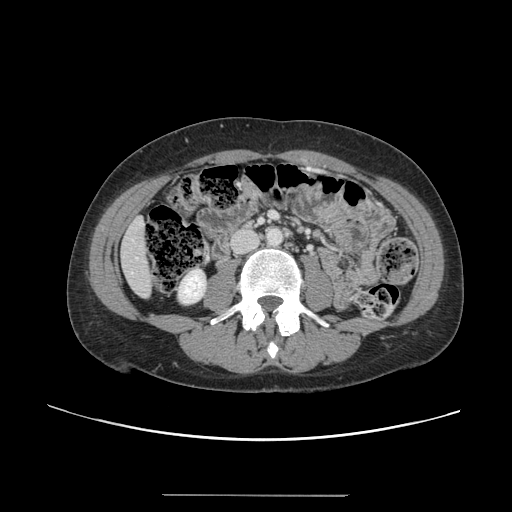
Contrast-enhanced abdominal CT, one axial slice; position 24 of 144 along the scan axis; intravenous contrast given; soft-tissue window (W 400 / L 40 HU); 2.5 mm slice thickness; 512 × 512 image matrix, field of view 380 × 380 mm. Female patient, age 53 years. From the clinical record (not read from this slice): diagnosis: colorectal cancer liver metastases, imaged before liver resection; multiple liver metastases: yes; largest metastasis: 1.1 cm; chemotherapy before resection: no.
Annotated regions visible in this slice (outlined manually by an expert reader):
- liver: bounding box (x1, y1, x2, y2) in pixels: (121, 216, 152, 297)
- planned liver remnant (the part of the liver to remain after resection): (121, 216, 152, 297)